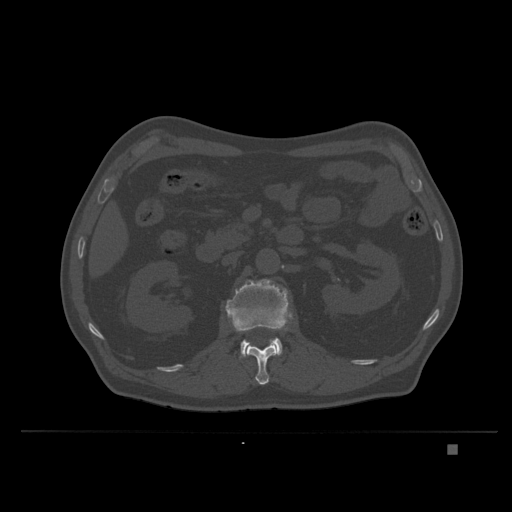
CT including the spine, one axial slice; position 128 of 435 along the scan axis; bone window (W 1800 / L 400 HU); 1.5 mm slice thickness; 512 × 512 image matrix. Patient: male, 73 years. From the clinical record (not read from this slice): primary cancer: skin.
Structures marked on this image (semi-automatic segmentation, software-assisted and operator-edited):
- L1 vertebra: bounding box [x1, y1, x2, y2] px = [246, 339, 277, 385]
- L2 vertebra: [225, 279, 293, 357]